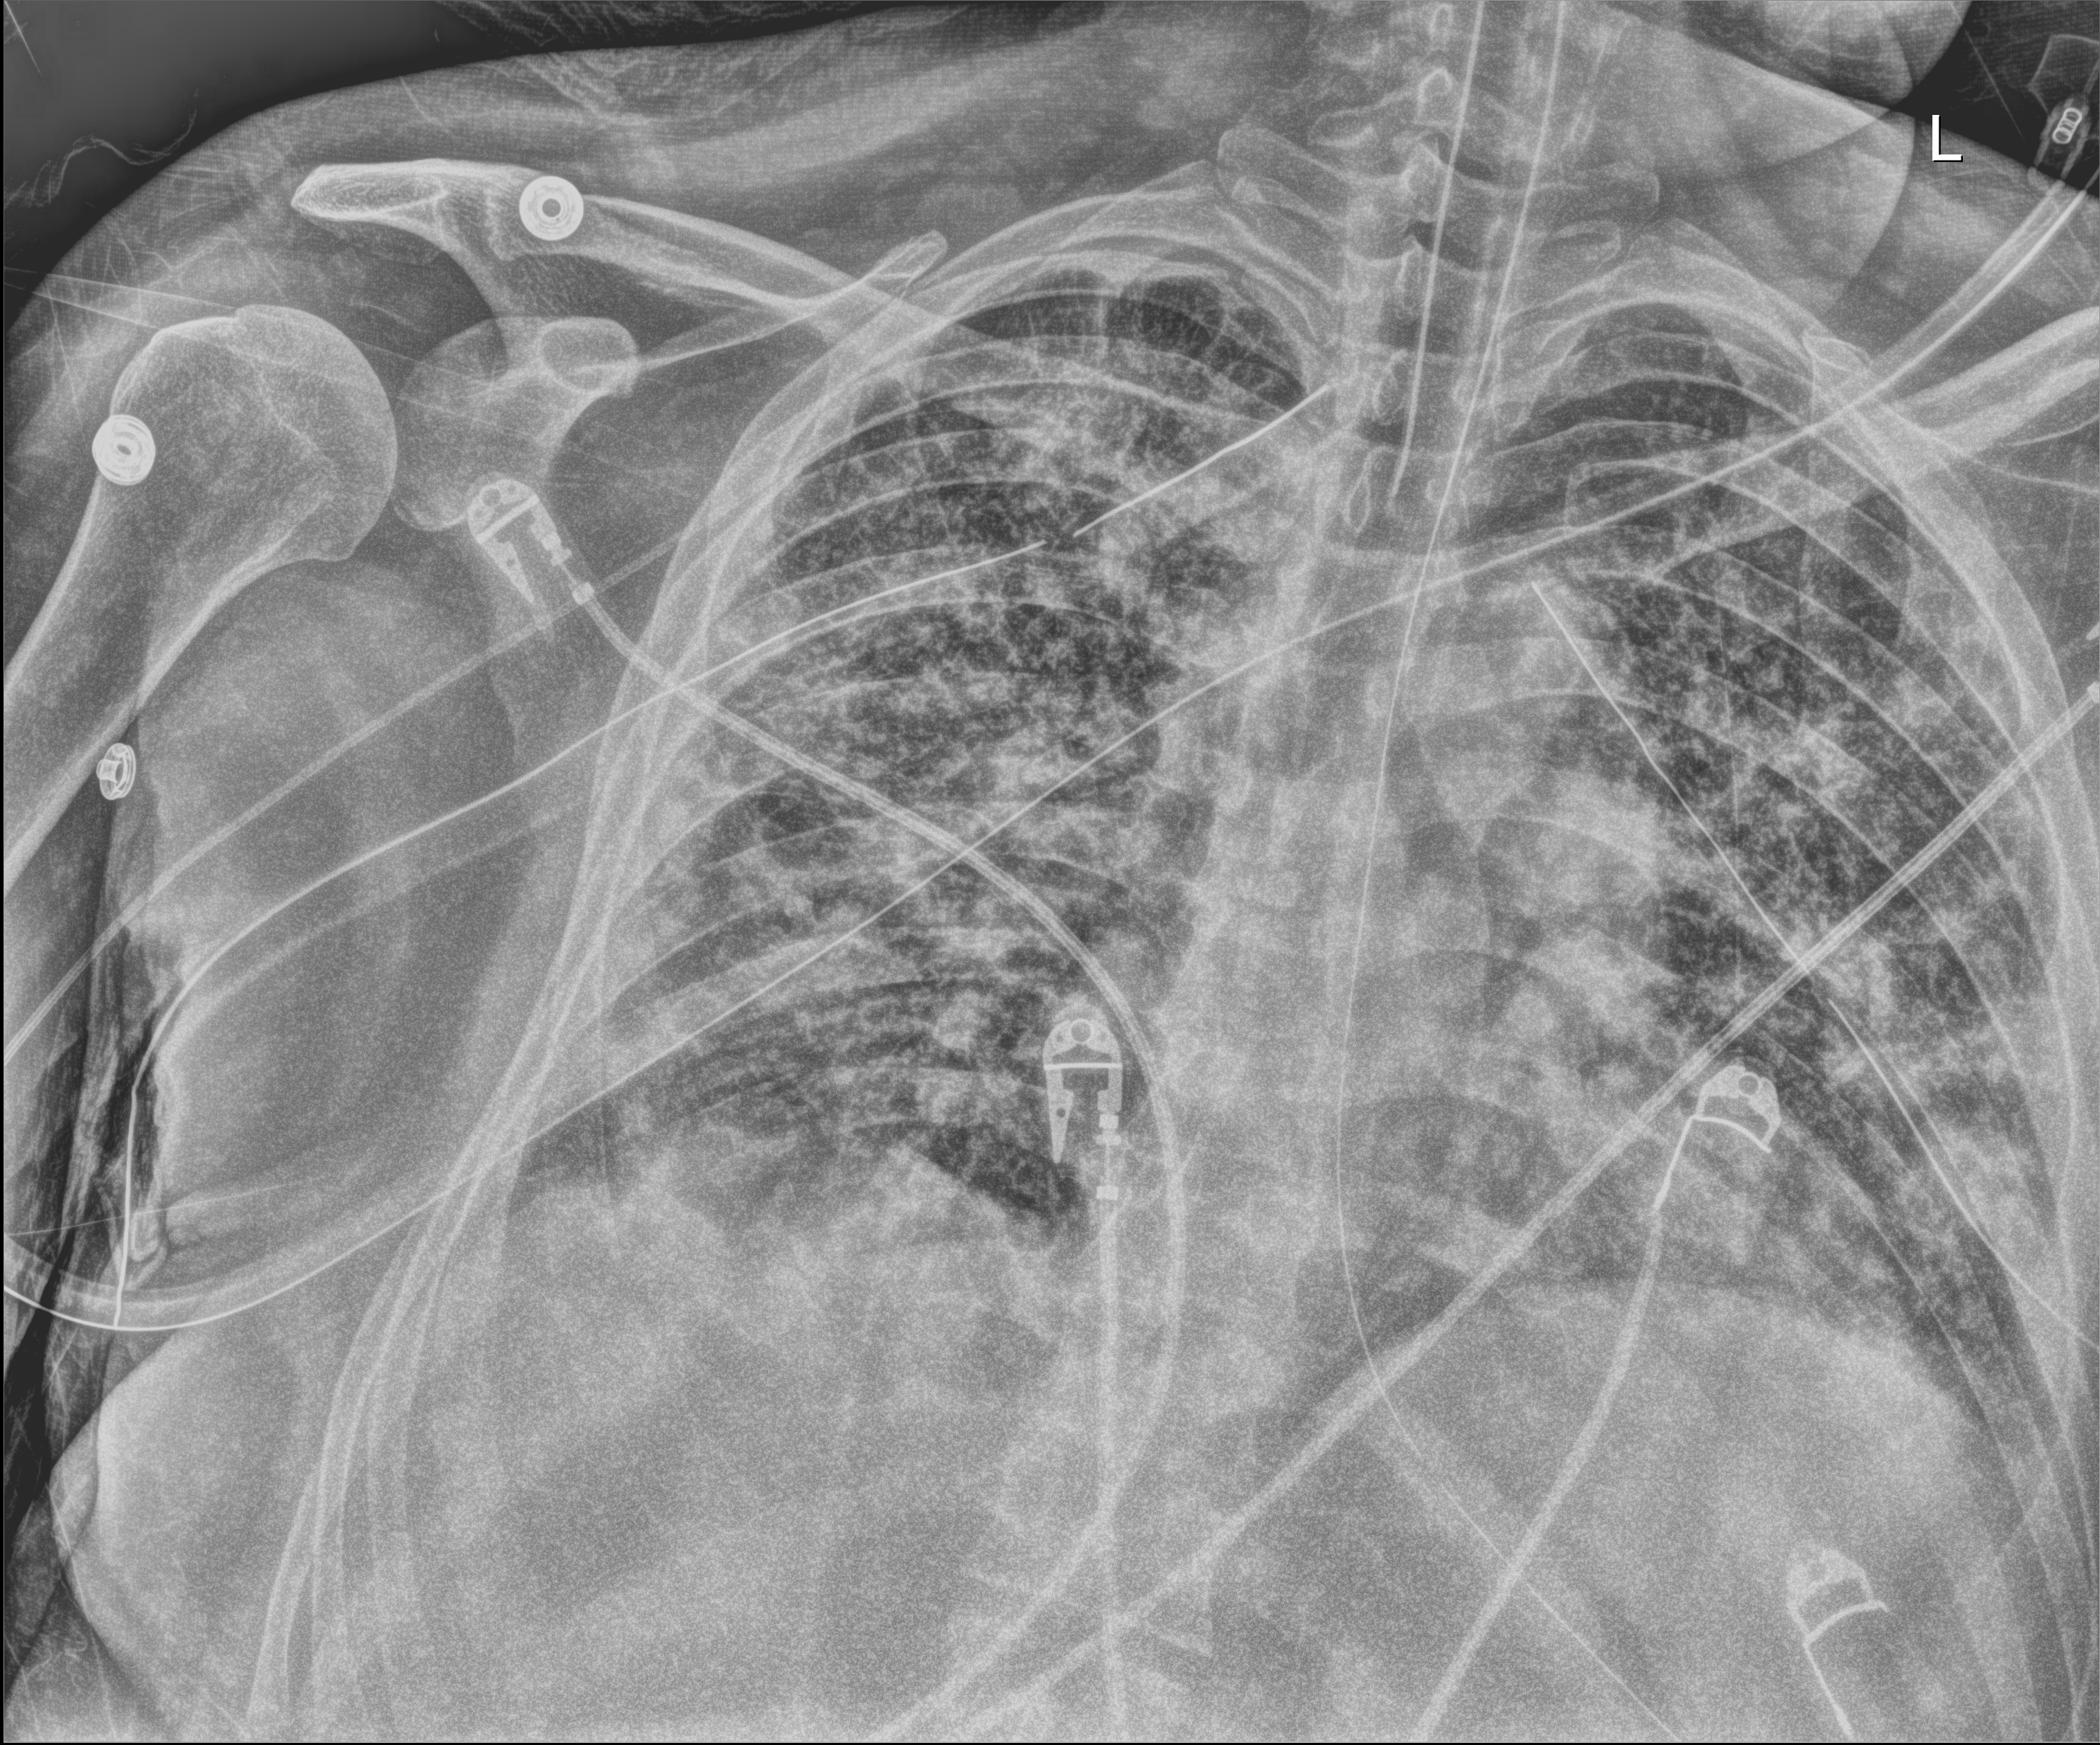
Bedside chest radiograph (digital radiography); anteroposterior (AP) projection. Male patient hospitalised with COVID-19, age 18–59 years.
Hospital-stay facts (about this admission, not read from this image; timing relative to this image not recorded):
- COPD (admission record): no
- smoking status (admission record): never
- length of hospital stay: 63 days